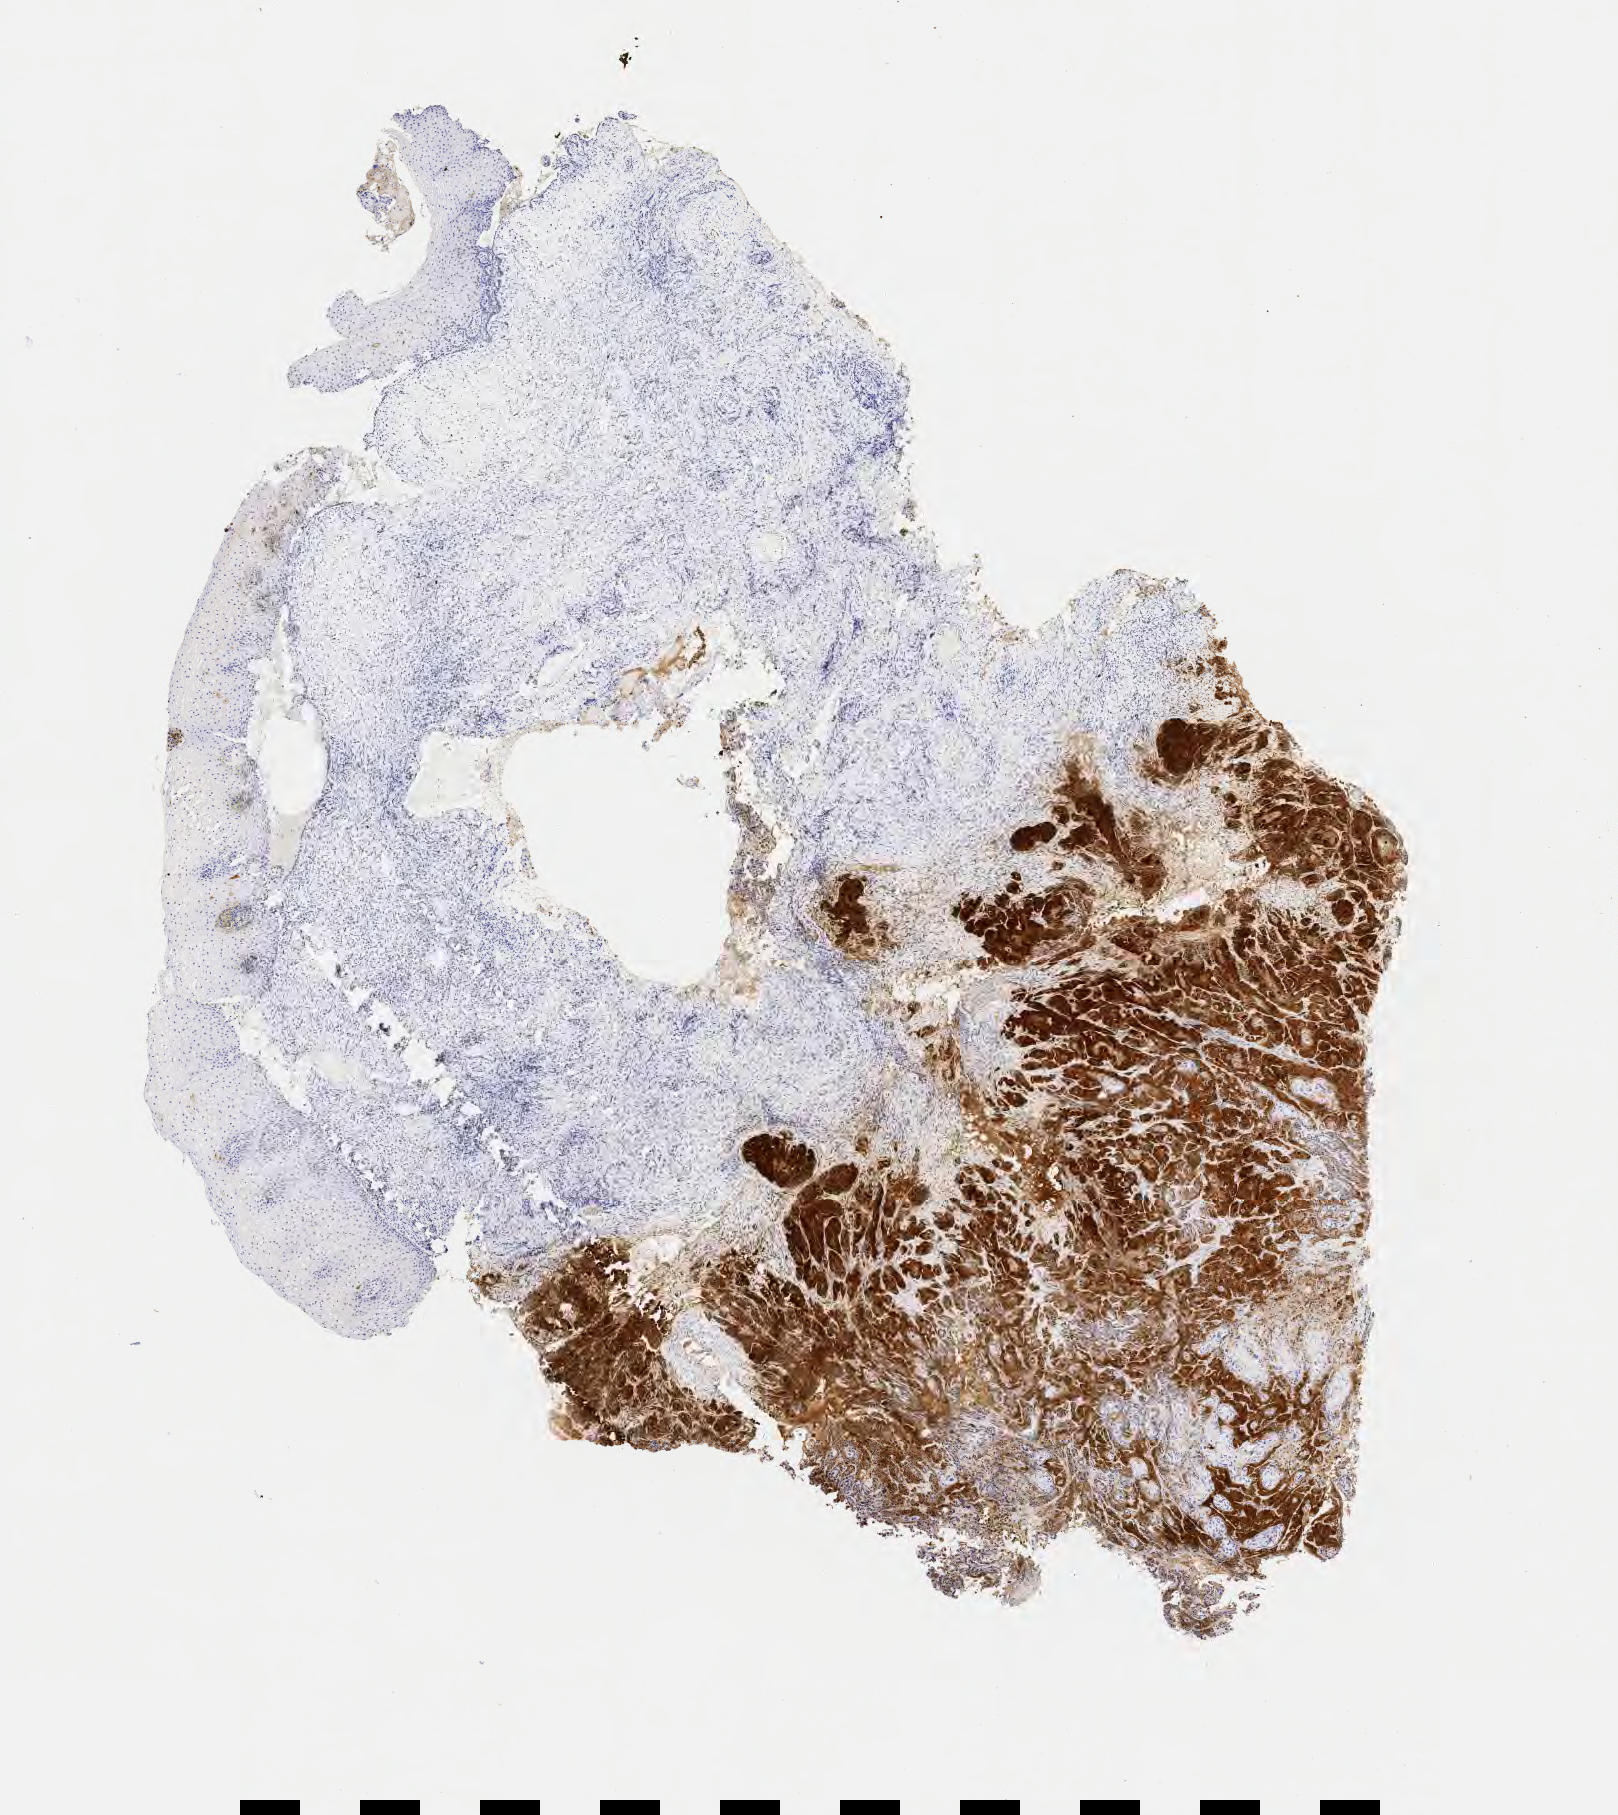
IHC for p16 (p16INK4a), whole-slide image, whole scanned area (about 6.5 x 7.3 mm) shown as a low-resolution overview. Specimen: tumor tissue. Anatomic site: cervix. Patient: female, aged 38.
- diagnosis: Squamous cell carcinoma, keratinizing, NOS